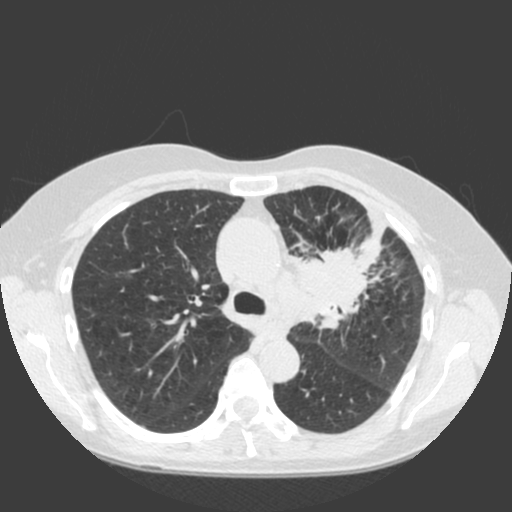
Low-dose screening chest CT, one axial slice. Position 130 of 184 along the scan axis. Lung window (W 1500 / L -600 HU). 2 mm slice thickness. 512 × 512 image matrix, field of view 350 × 350 mm.
Outlined on this slice (expert manual segmentation):
- lesion 1 (tumor, hilum of left lung): bounding box [x1, y1, x2, y2] px = [289, 211, 386, 327]